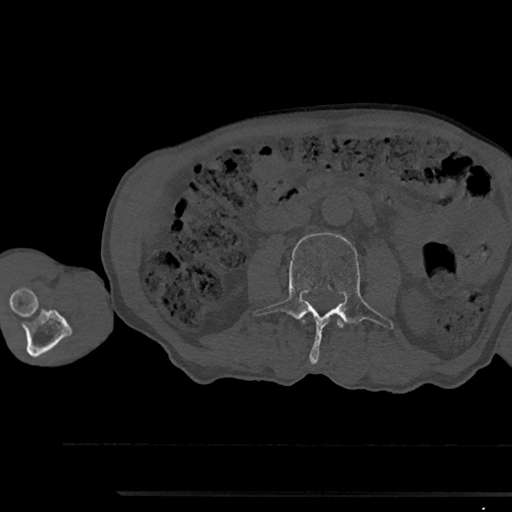
CT including the spine, one axial slice; position 498 of 797 along the scan axis; reconstruction kernel Br40s/3; bone window (W 1800 / L 400 HU); 0.5 mm slice thickness; 512 × 512 image matrix, field of view 367 × 367 mm. Patient: male, 79 years. From the clinical record (not read from this slice): primary cancer: prostate.
Outlined on this slice (semi-automatic segmentation, software-assisted and operator-edited):
- L2 vertebra: bounding box (x1, y1, x2, y2) in pixels: (303, 319, 343, 328)
- L3 vertebra: (253, 233, 393, 364)